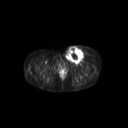
FDG PET of an extremity soft-tissue mass (from a PET/CT study), one axial slice; slice 58 of 267 in the series (ordered by position); 3.27 mm slice thickness; 128 × 128 image matrix, field of view 600 × 600 mm. Female patient, age 24 years. Case-level facts recorded for this patient, not image findings: histological type: leiomyosarcoma; grade: high; site of the primary tumour: groin.
Structures marked on this image (expert contour drawn on MRI and transferred to this co-registered scan by the dataset authors):
- gross tumour volume including surrounding oedema: box from (x=64, y=45) to (x=88, y=63) px
- gross tumour volume (mass): (x=65, y=46)–(x=84, y=63)